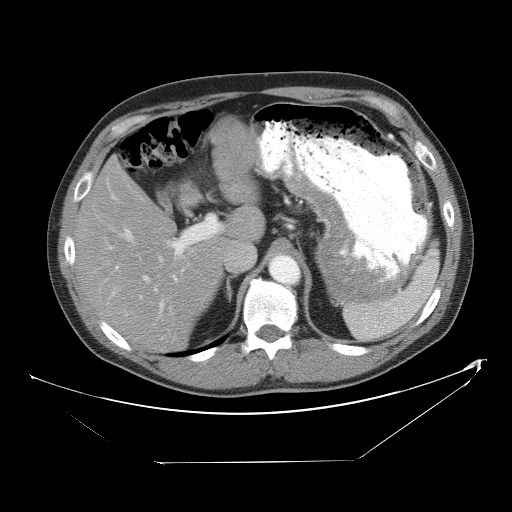
Contrast-enhanced abdominal CT, one axial slice. Slice 35 of 53 in the series (ordered by position). Reconstruction kernel STANDARD. 120 kVp. Intravenous contrast given. Soft-tissue window (W 400 / L 40 HU). 512 × 512 image matrix. Male patient, age 59 years. From the clinical record (not read from this slice): diagnosis: colorectal cancer liver metastases, imaged before liver resection; multiple liver metastases: yes; largest metastasis: 8.5 cm; disease in both lobes: no.
Structures marked on this image (manually delineated by an expert):
- hepatic veins: box from (x=119, y=227) to (x=185, y=292) px
- liver: (x=77, y=123)–(x=263, y=352)
- planned liver remnant (the part of the liver to remain after resection): (x=77, y=160)–(x=229, y=352)
- portal vein (with intrahepatic branches): (x=110, y=217)–(x=217, y=298)